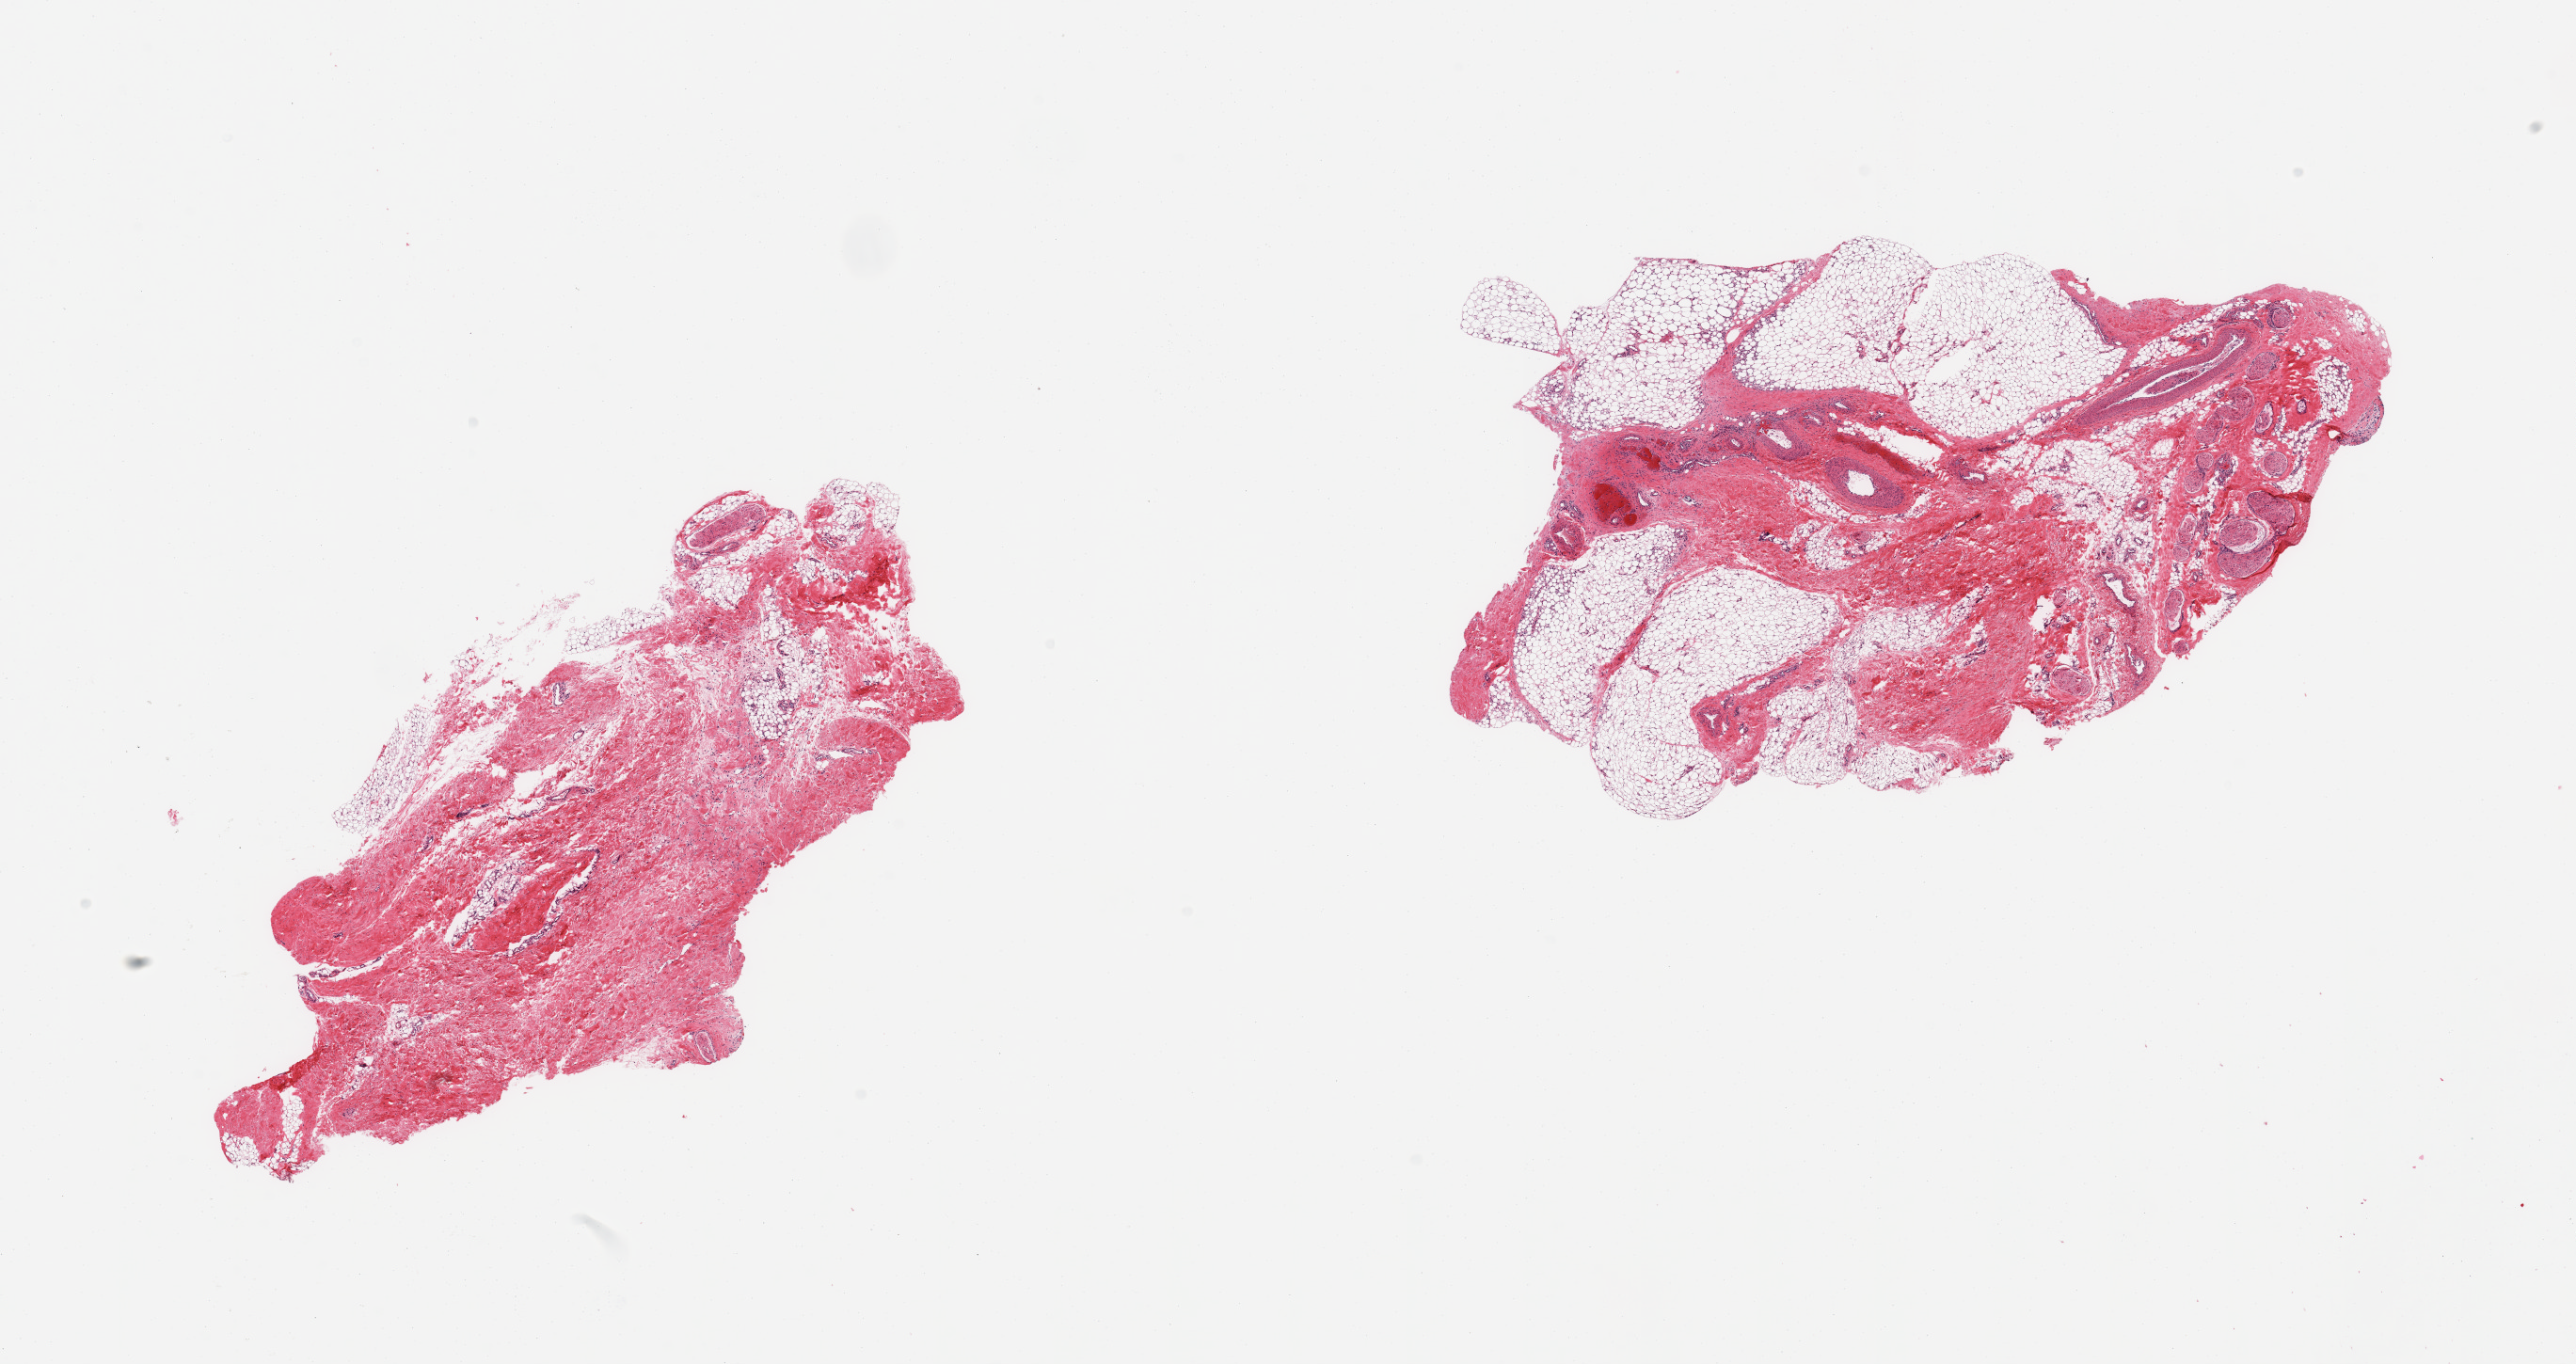
Whole-slide image, H&E stain, low-resolution overview of the scanned area, about 21.7 x 11.5 mm (slide scanned at 20x). PAXgene-fixed paraffin-embedded (PFPE) section. Target tissue: breast. Donor tissue sample.
Pathologist's review note for this sample: 2 pieces, fibroadipose and abundant peripheral nerve (, rep) elements.